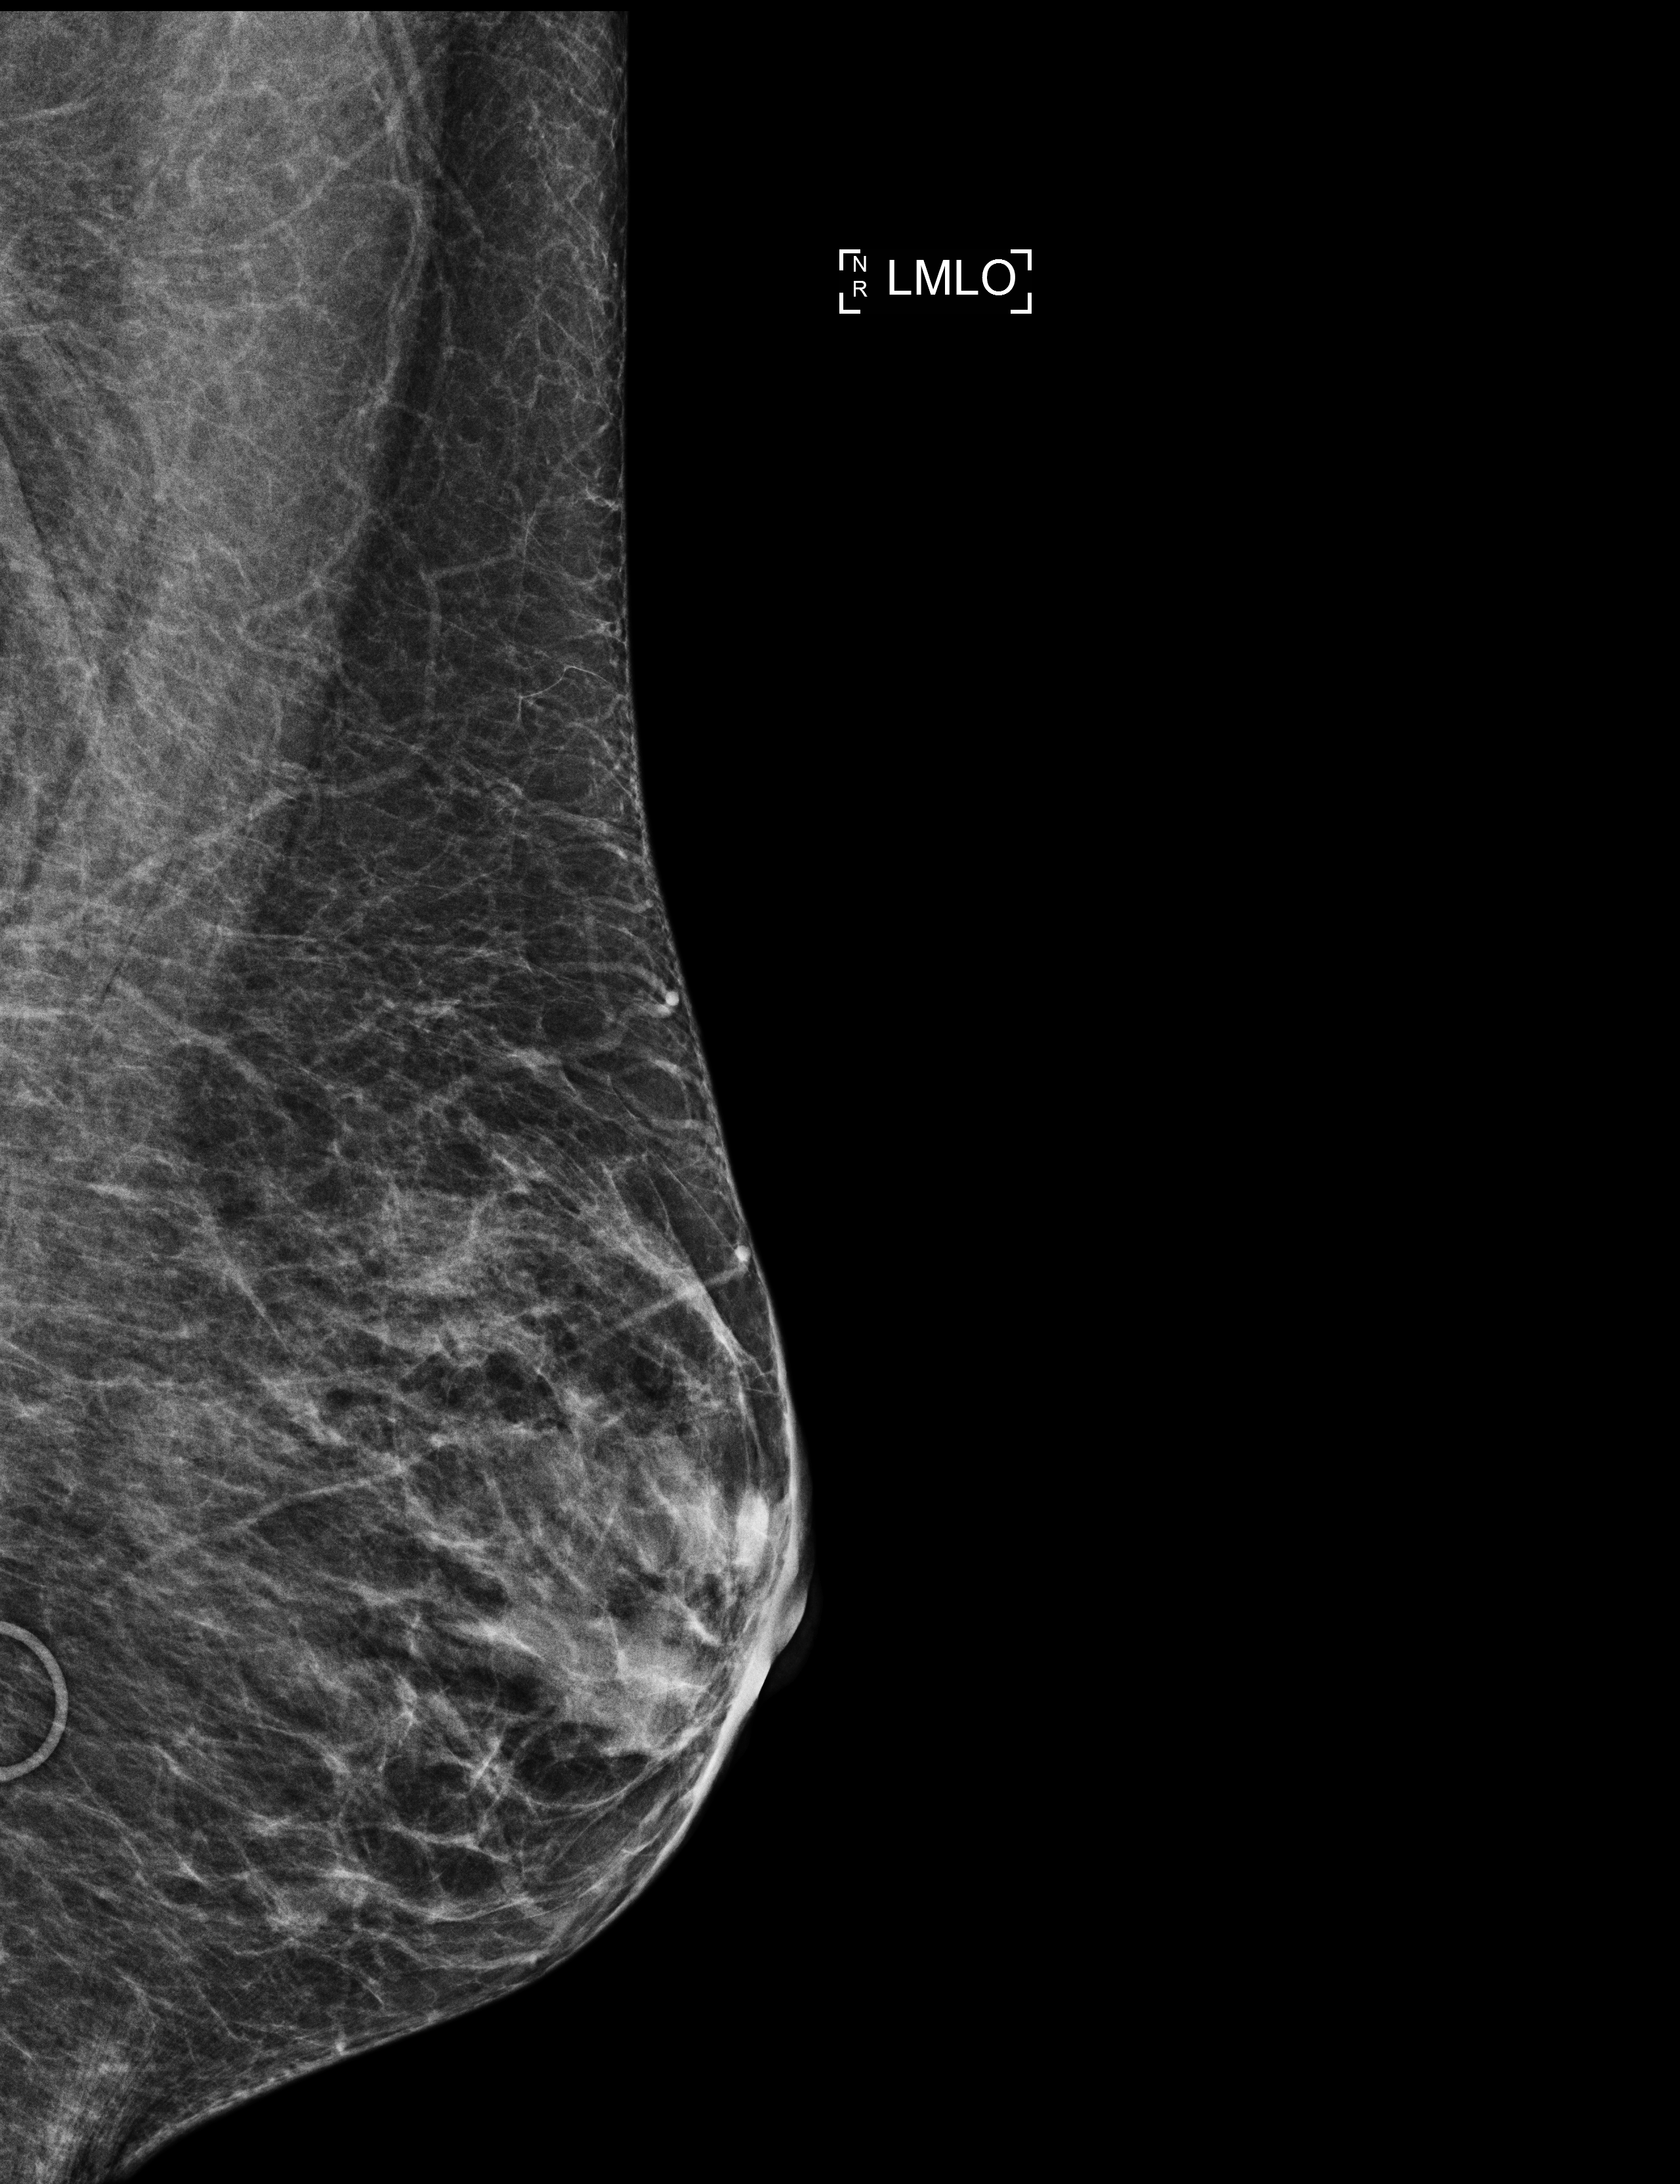
Full-field digital mammogram (FFDM); left breast; MLO view; screening examination; compressed breast thickness 29 mm; system: Selenia Dimensions. Patient aged 59 years (female).
BI-RADS breast density category at the screening exam (both breasts, scale 1–4): 2.